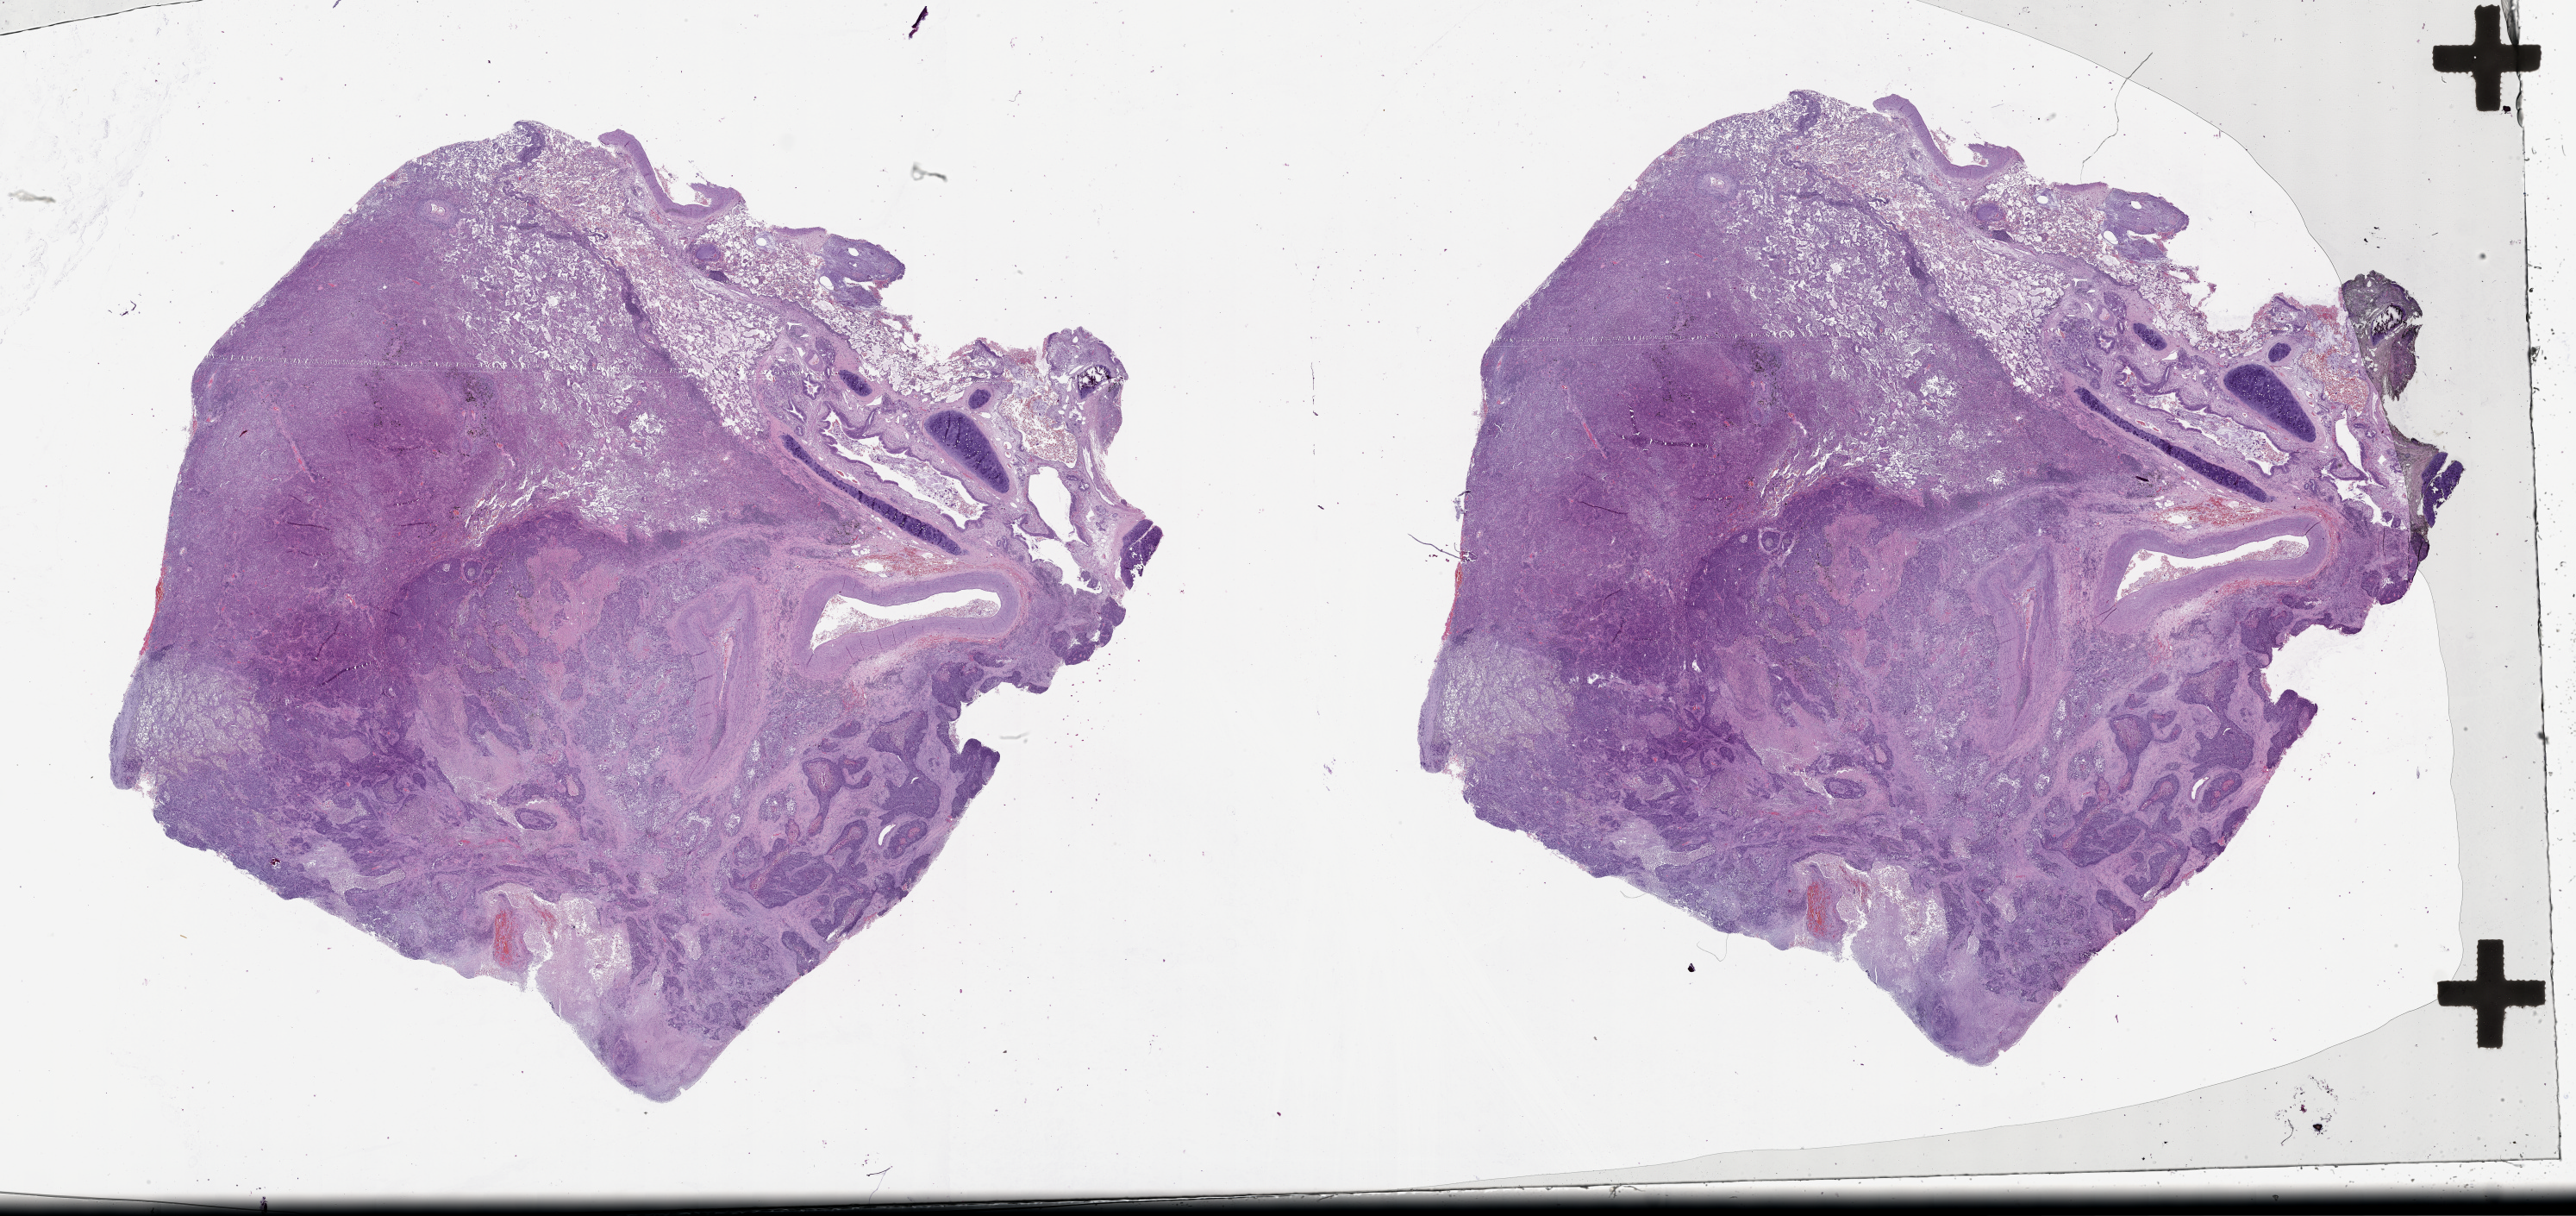
Digitized H&E tissue section (whole slide) — low-resolution overview of the scanned area, about 48.1 x 22.7 mm, lung, tissue type not recorded.
Patient diagnosis (cohort enrolment): squamous cell carcinoma (lung).